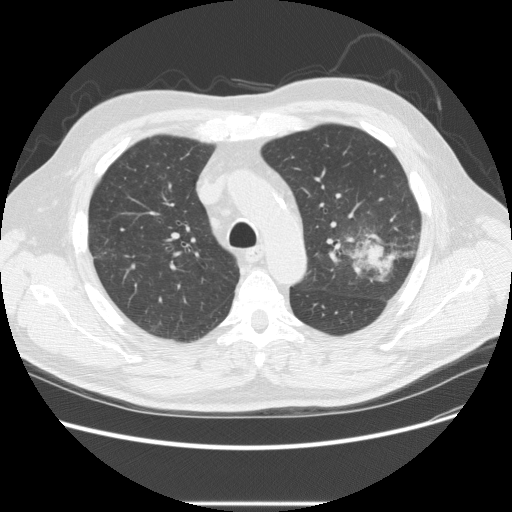
Axial slice from a low-dose chest CT screening exam. Baseline annual screen. Lung window (W 1500 / L -600 HU). Male participant, aged 73 years at enrolment. Former smoker at enrolment.
• Expert reader's lesion annotation, bounding box (x1, y1, x2, y2) in pixels: (332, 215, 419, 287).
• The screening reader recorded 2 non-calcified nodules or masses ≥4 mm on this exam (left upper lobe, right upper lobe); which of them this box marks is not recorded.
• Official screen result: positive, change unspecified: nodule(s) >= 4 mm or enlarging nodule(s), mass(es), or other non-specific abnormalities suspicious for lung cancer.
• Participant outcome: lung cancer diagnosed 11 days after this screen — bronchiolo-alveolar adenocarcinoma, NOS, other location, well differentiated (G1), stage IV (AJCC 6th edition).